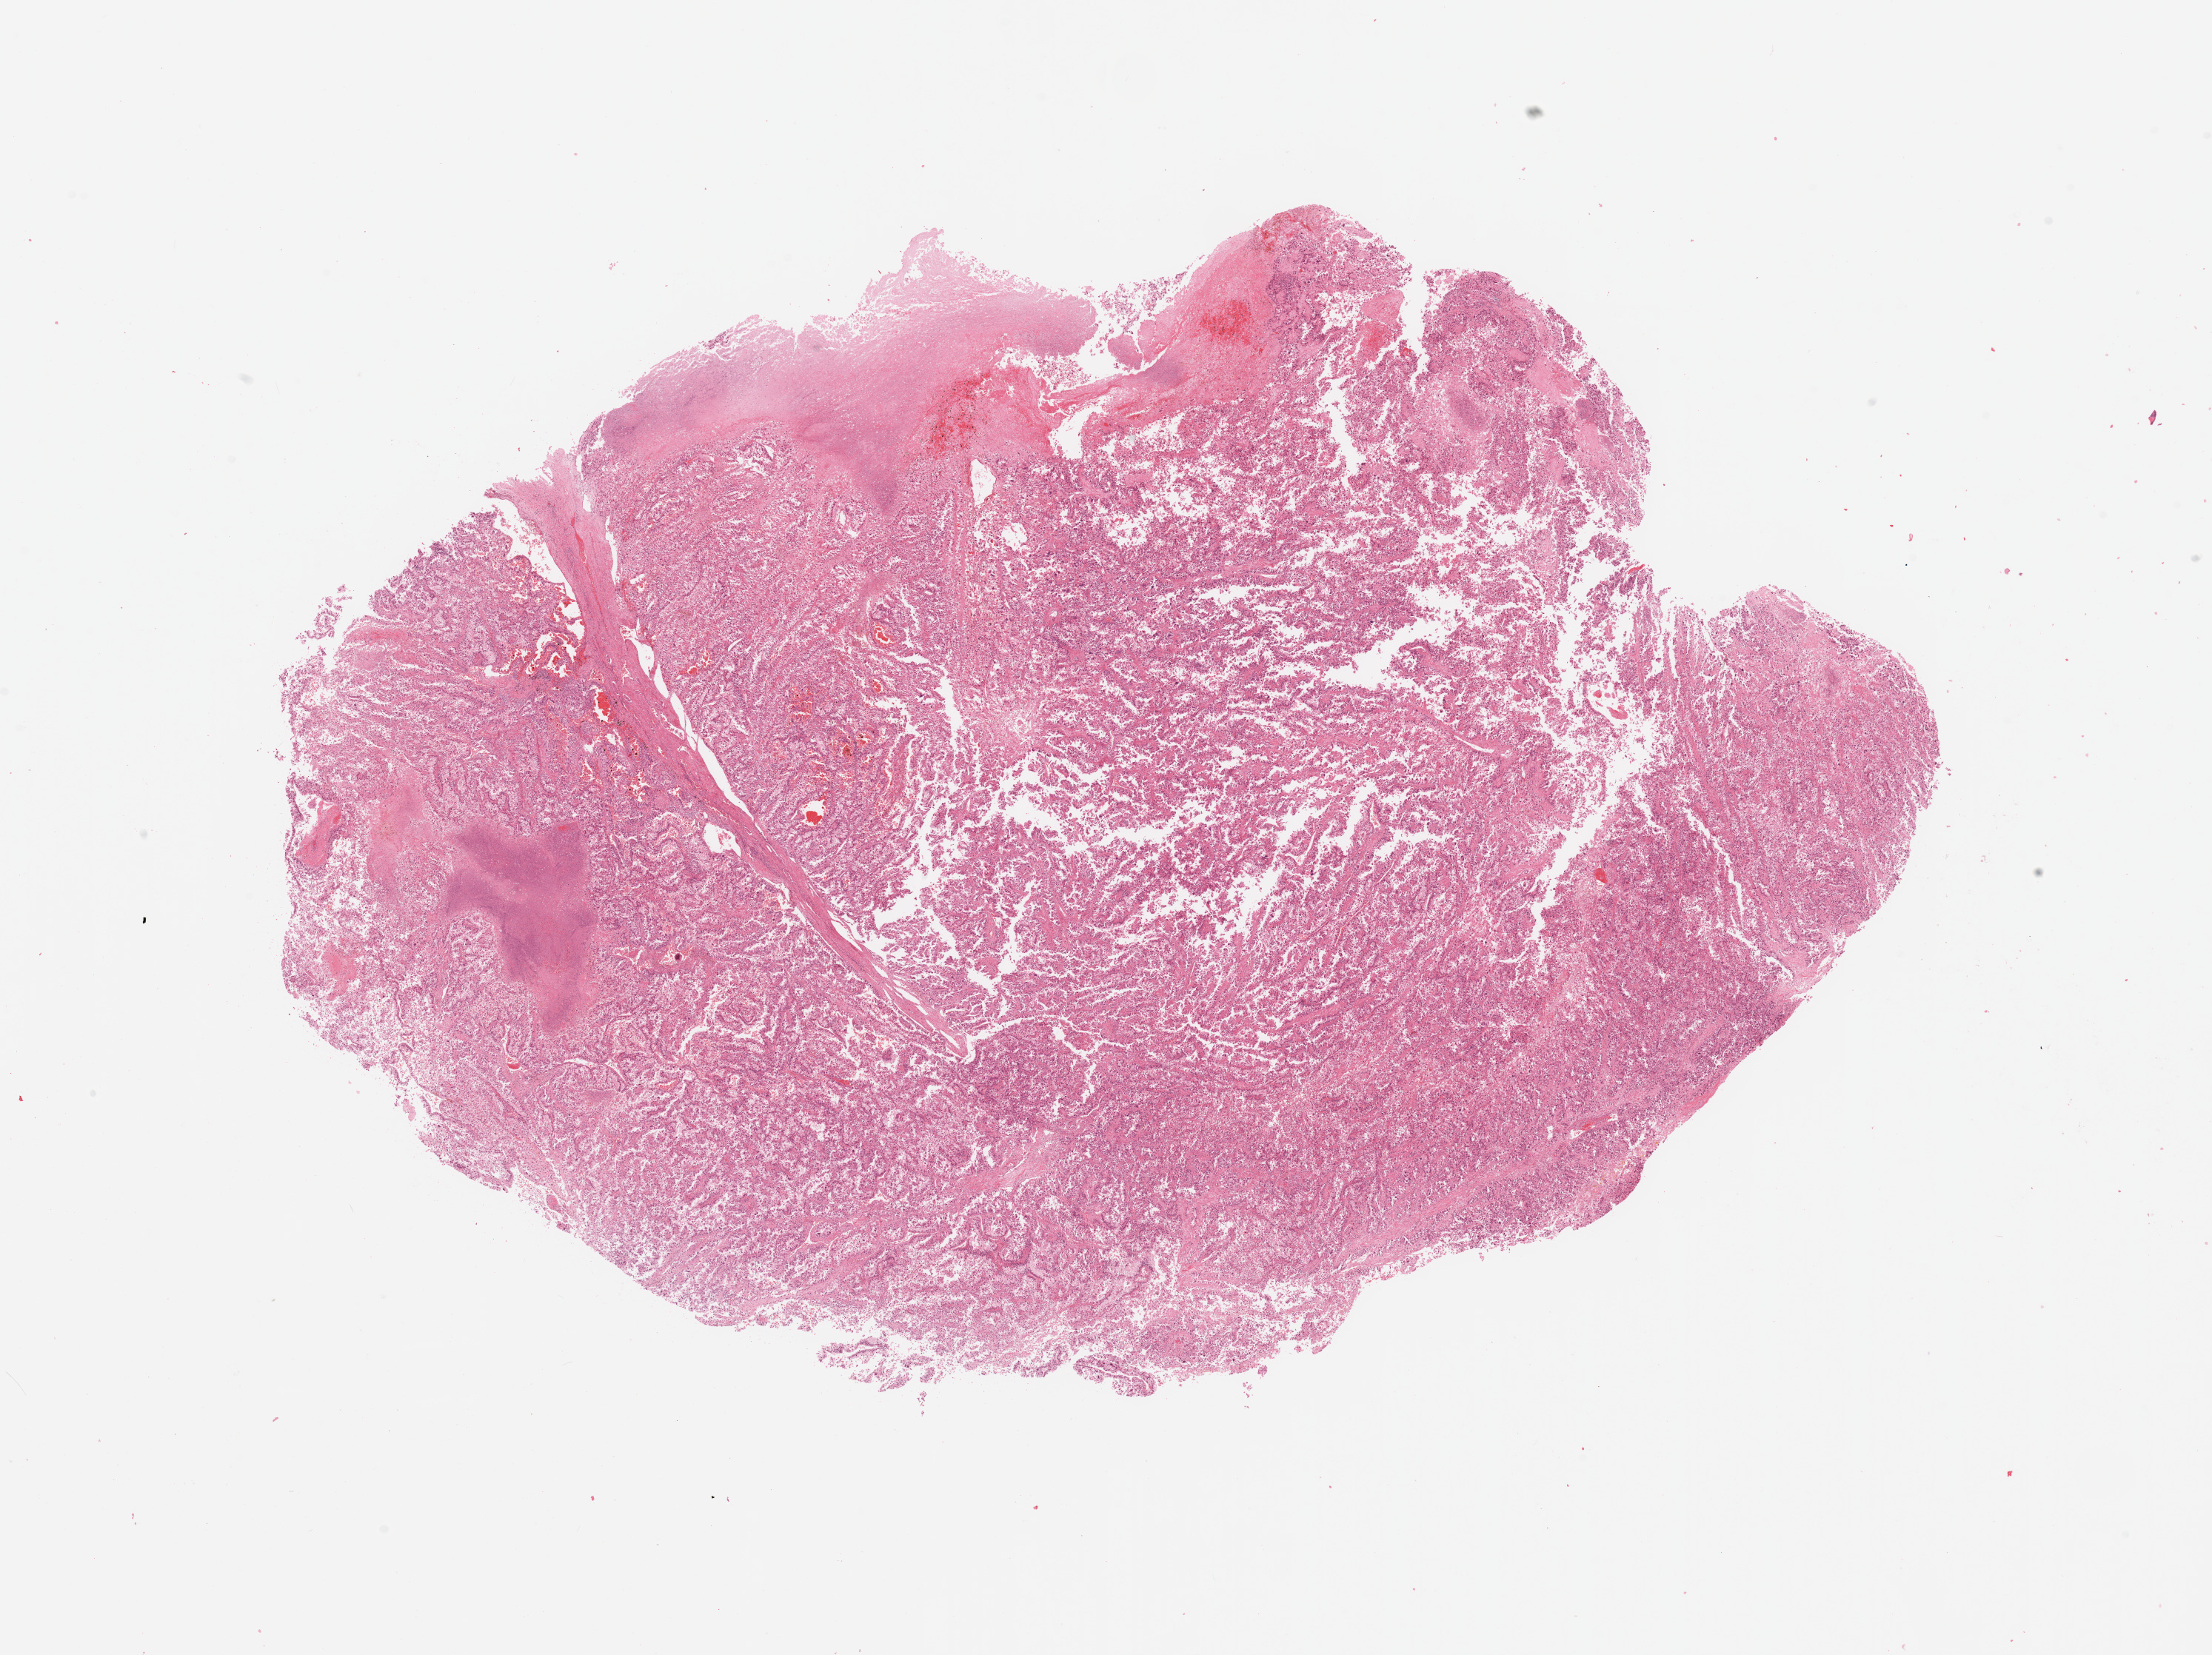
Hematoxylin and eosin (H&E) stained whole-slide image, shown as a low-resolution overview of the whole scanned area (about 23.6 x 17.7 mm, from a 20x scan); tumour tissue sample, kidney. 68-year-old female patient. Histologic grade: G3 (poorly differentiated).
* histologic diagnosis: Renal cell carcinoma, NOS